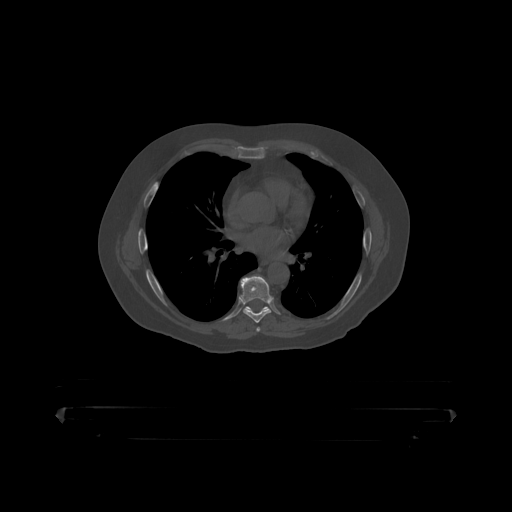
CT including the spine, one axial slice; slice 275 of 390 in the series (ordered by position); reconstruction kernel STANDARD; bone window (W 1800 / L 400 HU); 512 × 512 image matrix, field of view 650 × 650 mm. Male patient, age 60 years. From the clinical record (not read from this slice): primary cancer: prostate.
Outlined on this slice (semi-automatic segmentation, software-assisted and operator-edited):
- T7 vertebra: bounding box (x1, y1, x2, y2) in pixels: (240, 276, 273, 319)
- T8 vertebra: (246, 307, 269, 310)